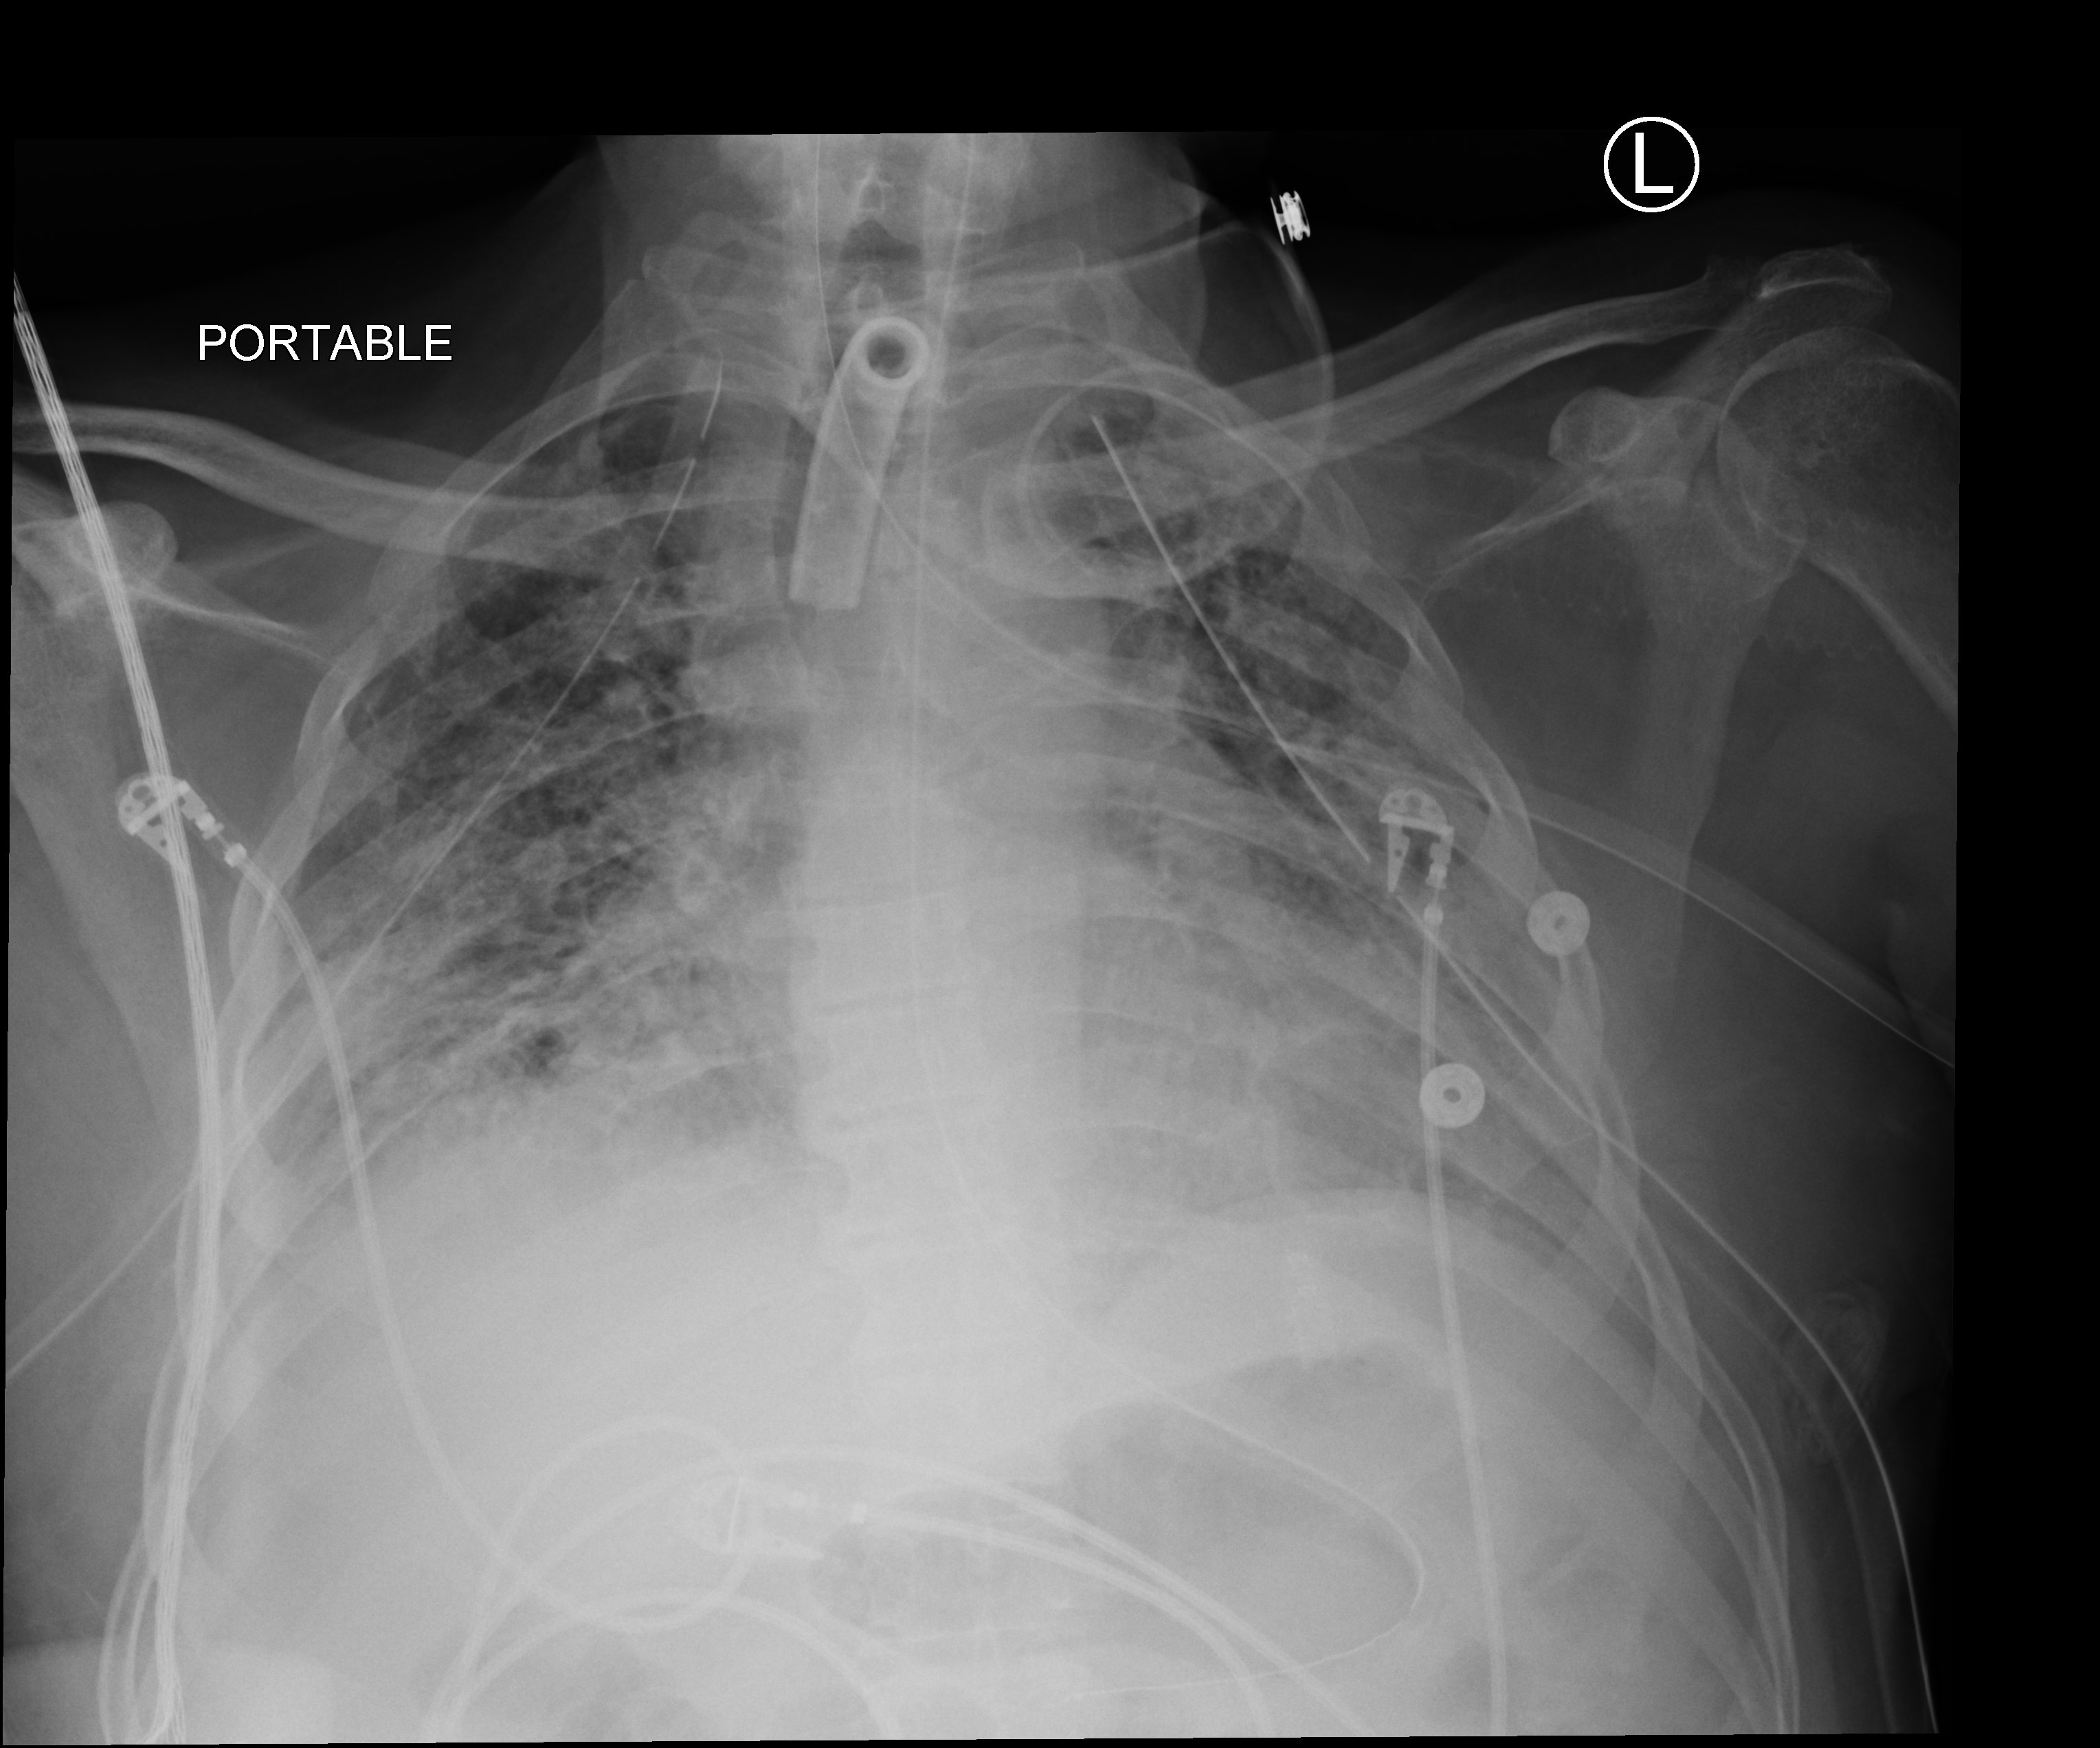
Portable chest radiograph. Male patient hospitalised with COVID-19, age 18–59 years.
Hospital-stay facts (about this admission, not read from this image; timing relative to this image not recorded): mechanically ventilated during this hospital stay: yes; admitted to intensive care during this hospital stay: yes.